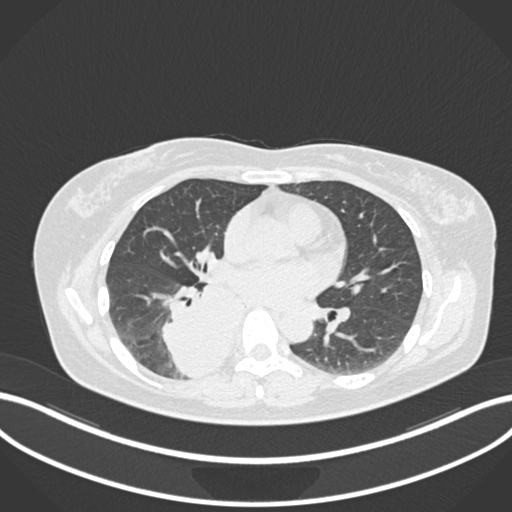
Chest CT, one axial slice; position 583 of 677 along the scan axis; lung window (W 1500 / L -600 HU); 1 mm slice thickness; 512 × 512 image matrix. Female patient, age 54 years. Case-level facts recorded for this patient, not image findings: clinical TNM (as recorded): T4 N0 M0.
Structures marked on this image (rectangle marked by the reading radiologist):
- lung tumour (recorded histology: adenocarcinoma): bounding box (x1, y1, x2, y2) in pixels: (153, 274, 248, 382)